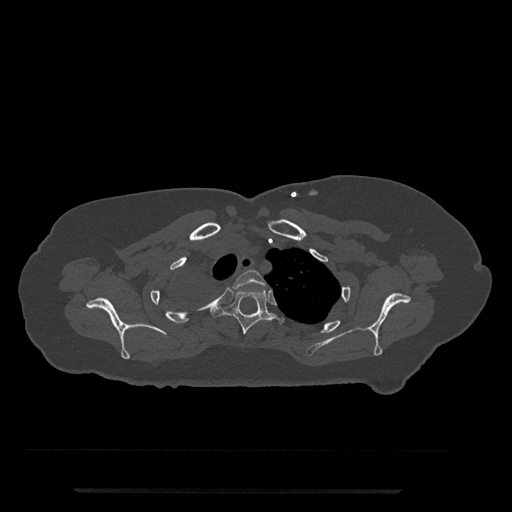
CT including the spine, one axial slice; position 639 of 797 along the scan axis; reconstruction kernel Br40s/3; bone window (W 1800 / L 400 HU); 0.5 mm slice thickness; 512 × 512 image matrix, field of view 440 × 440 mm. Patient: female, 51 years. Case-level facts recorded for this patient, not image findings: primary cancer: neuro.
Outlined on this slice (semi-automatically segmented with operator editing):
- T2 vertebra: box from (x=233, y=270) to (x=266, y=290) px
- T3 vertebra: (x=213, y=289)–(x=283, y=335)